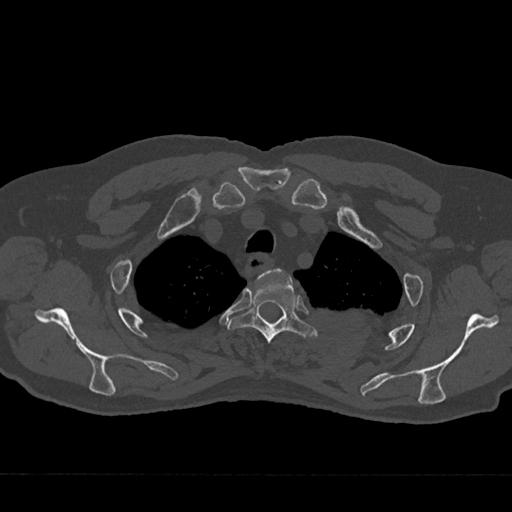
CT including the spine, one axial slice; slice 575 of 797 in the series (ordered by position); reconstruction kernel Br40s/3; 120 kVp; bone window (W 1800 / L 400 HU); 0.5 mm slice thickness; 512 × 512 image matrix, field of view 377 × 377 mm. Male patient, age 75 years. From the clinical record (not read from this slice): primary cancer: renal; vertebrae with lytic lesions (as recorded): T4.
Outlined on this slice (semi-automatically segmented with operator editing):
- T2 vertebra: bounding box (x1, y1, x2, y2) in pixels: (257, 269, 283, 281)
- T3 vertebra: (229, 278, 317, 343)